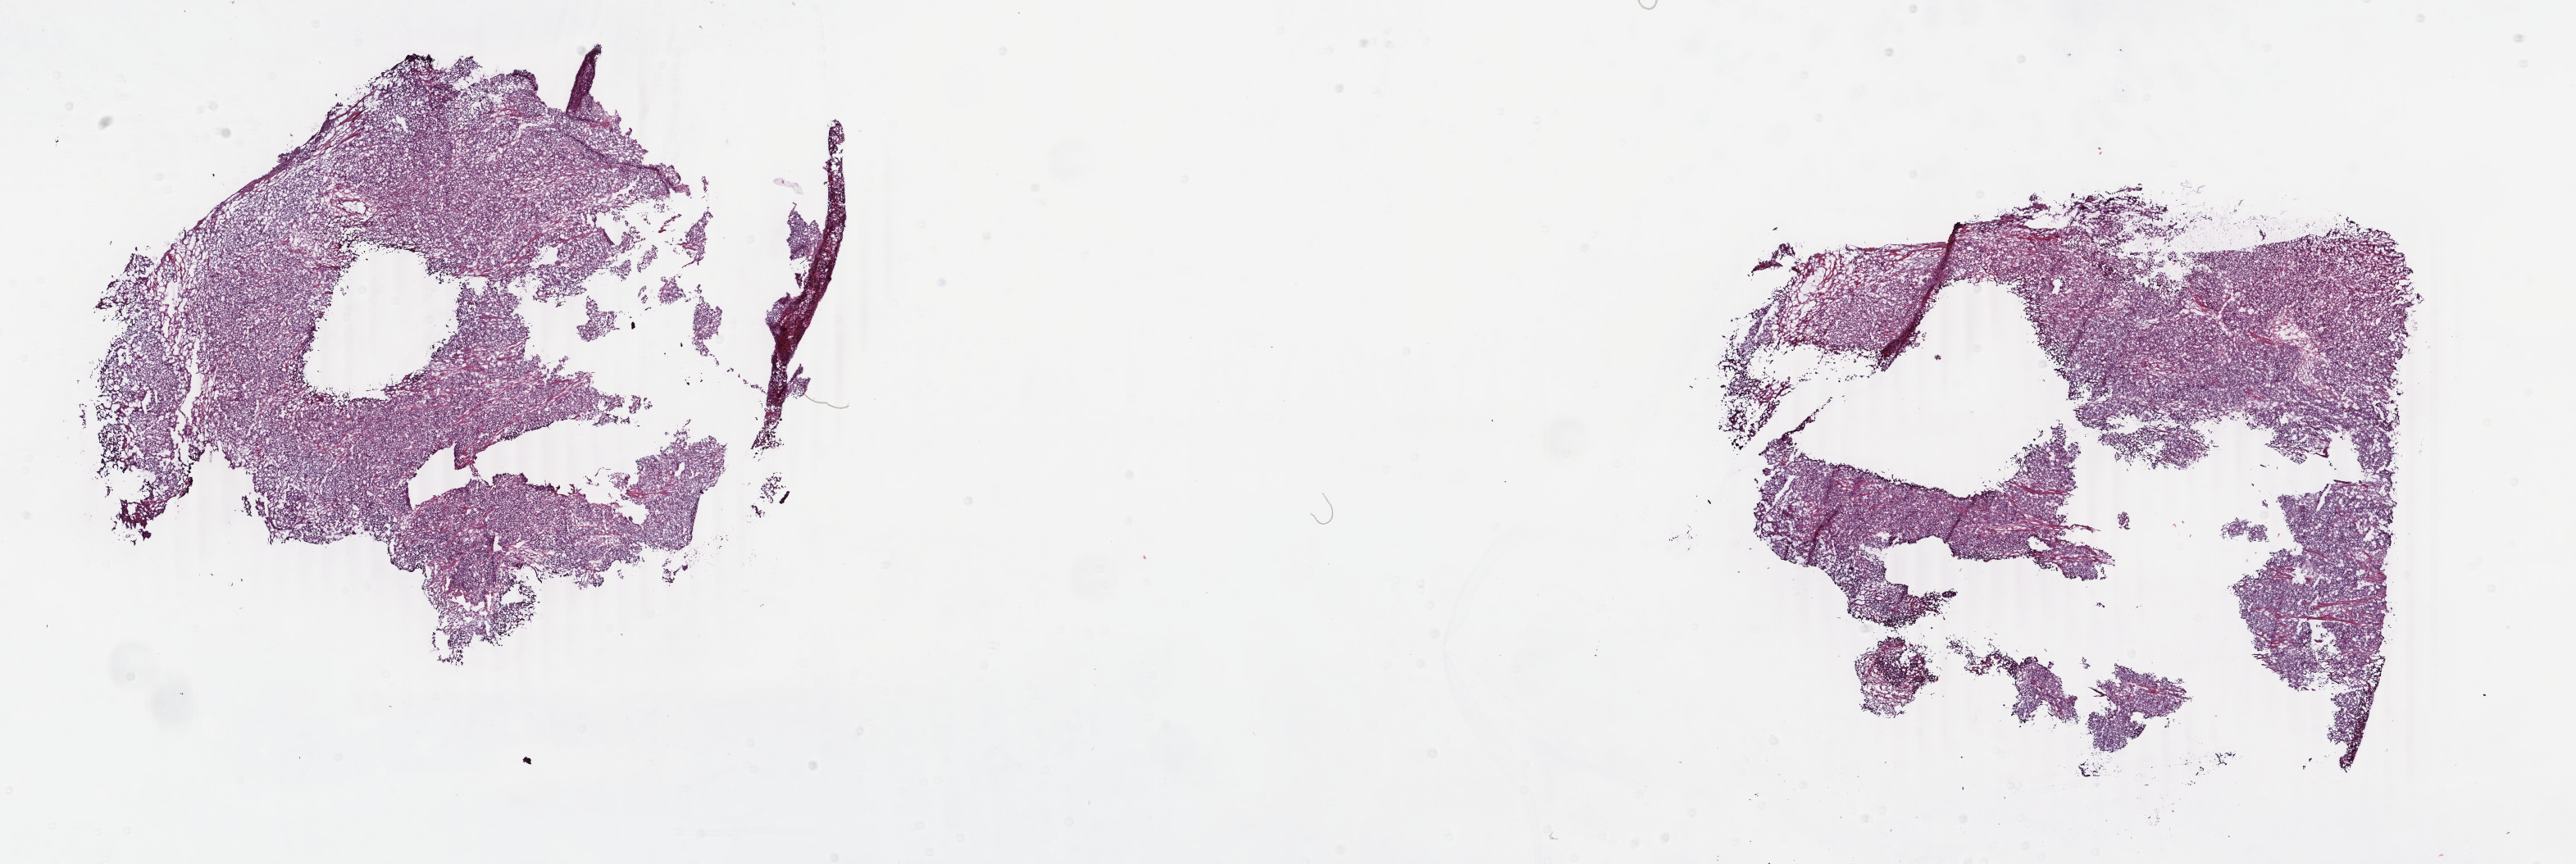
H&E whole-slide image, low-resolution overview of the scanned area, about 25.0 x 8.4 mm, frozen section, sample: primary tumour, uterus. Patient: female, age at initial diagnosis 59 years. Histologic grade: G3 (poorly differentiated). Slide review estimates, as recorded: tumour cells 80%, tumour nuclei 90%, normal cells 10%, stromal cells 2%, necrosis 8%. Infiltration values recorded for this section: lymphocyte infiltration 0%, monocyte infiltration 0%, neutrophil infiltration 0%.
Pathologic diagnosis: Endometrioid adenocarcinoma, NOS. Lymph nodes positive (case pathology): 2 of 16 examined. FIGO stage: IVA.